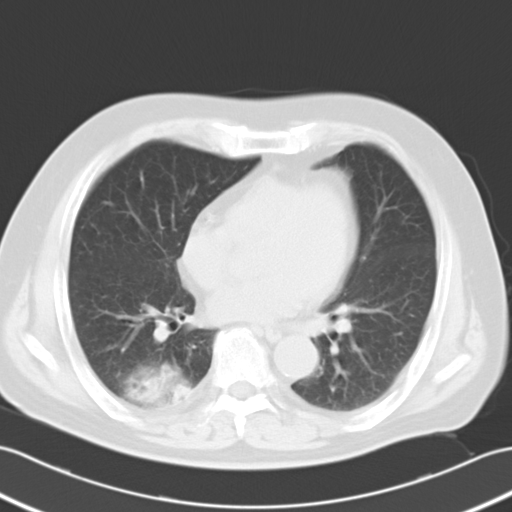
Chest CT, one axial slice. Position 9 of 25 along the scan axis. Reconstruction kernel B40f. 120 kVp. Lung window (W 1500 / L -600 HU). 10 mm slice thickness. 512 × 512 image matrix. Patient: male, 70 years. From the clinical record (not read from this slice): clinical TNM (as recorded): T2 N0 M0; histopathological grade: G2.
Annotated regions visible in this slice (rectangle marked by the reading radiologist):
- lung tumour (recorded histology: adenocarcinoma): bounding box [x1, y1, x2, y2] px = [131, 368, 193, 418]